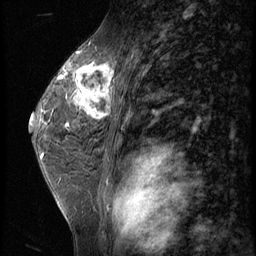
Breast MRI (dynamic contrast-enhanced), one sagittal slice; position 38 of 62 along the scan axis; 3 images stored at this slice position (order not interpretable as contrast timing); 1.5 T; TE 4.2 ms, TR 9 ms; 2.5 mm slice thickness; 256 × 256 image matrix, field of view 180 × 180 mm. Patient: female, 44 years. Case-level facts recorded for this patient, not image findings: setting: breast cancer imaged before/during neoadjuvant chemotherapy; receptor status: triple-negative.
Outlined on this slice (semi-automatically segmented with operator editing):
- analysis volume of interest (the breast-tissue region the enhancement analysis was run in; not a lesion): box from (x=69, y=64) to (x=116, y=125) px
- tumour enhancement mask (voxels above the 140 % enhancement threshold inside the analysis volume of interest): (x=71, y=64)–(x=115, y=120)